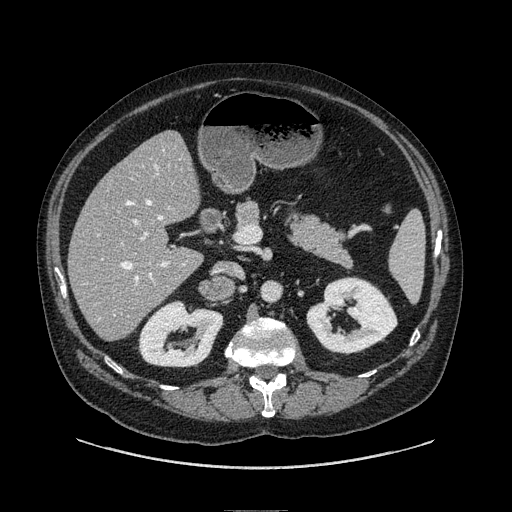
Contrast-enhanced abdominal CT, one axial slice. Slice 34 of 149 in the series (ordered by position). Soft-tissue window (W 400 / L 40 HU). 512 × 512 image matrix, field of view 440 × 440 mm. Male patient. Case-level facts recorded for this patient, not image findings: diagnosis: adrenocortical carcinoma; tumour side: right adrenal.
Annotated regions visible in this slice (semi-automatically segmented with operator editing):
- mass: bounding box (x1, y1, x2, y2) in pixels: (201, 280, 233, 297)